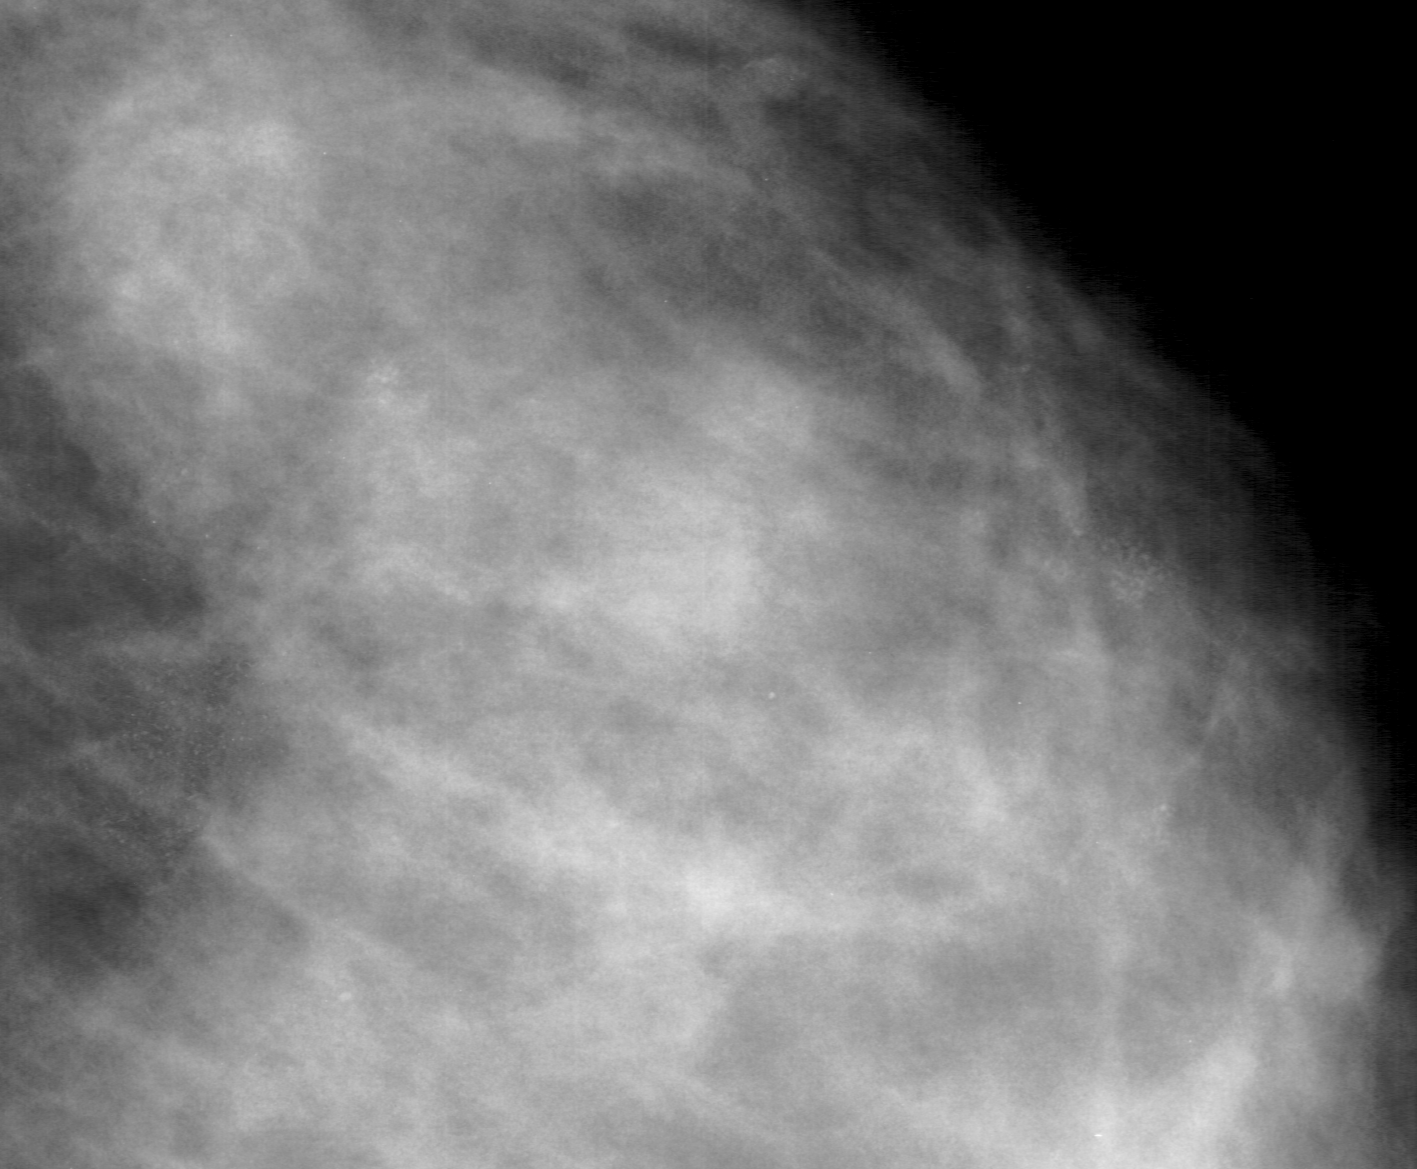
Cropped region of a digitized screen-film mammogram centred on a radiologist-marked abnormality, right breast, CC view.
- Marked abnormality: calcifications, morphology pleomorphic, distribution segmental; BI-RADS assessment category 4; pathology (as recorded): malignant.